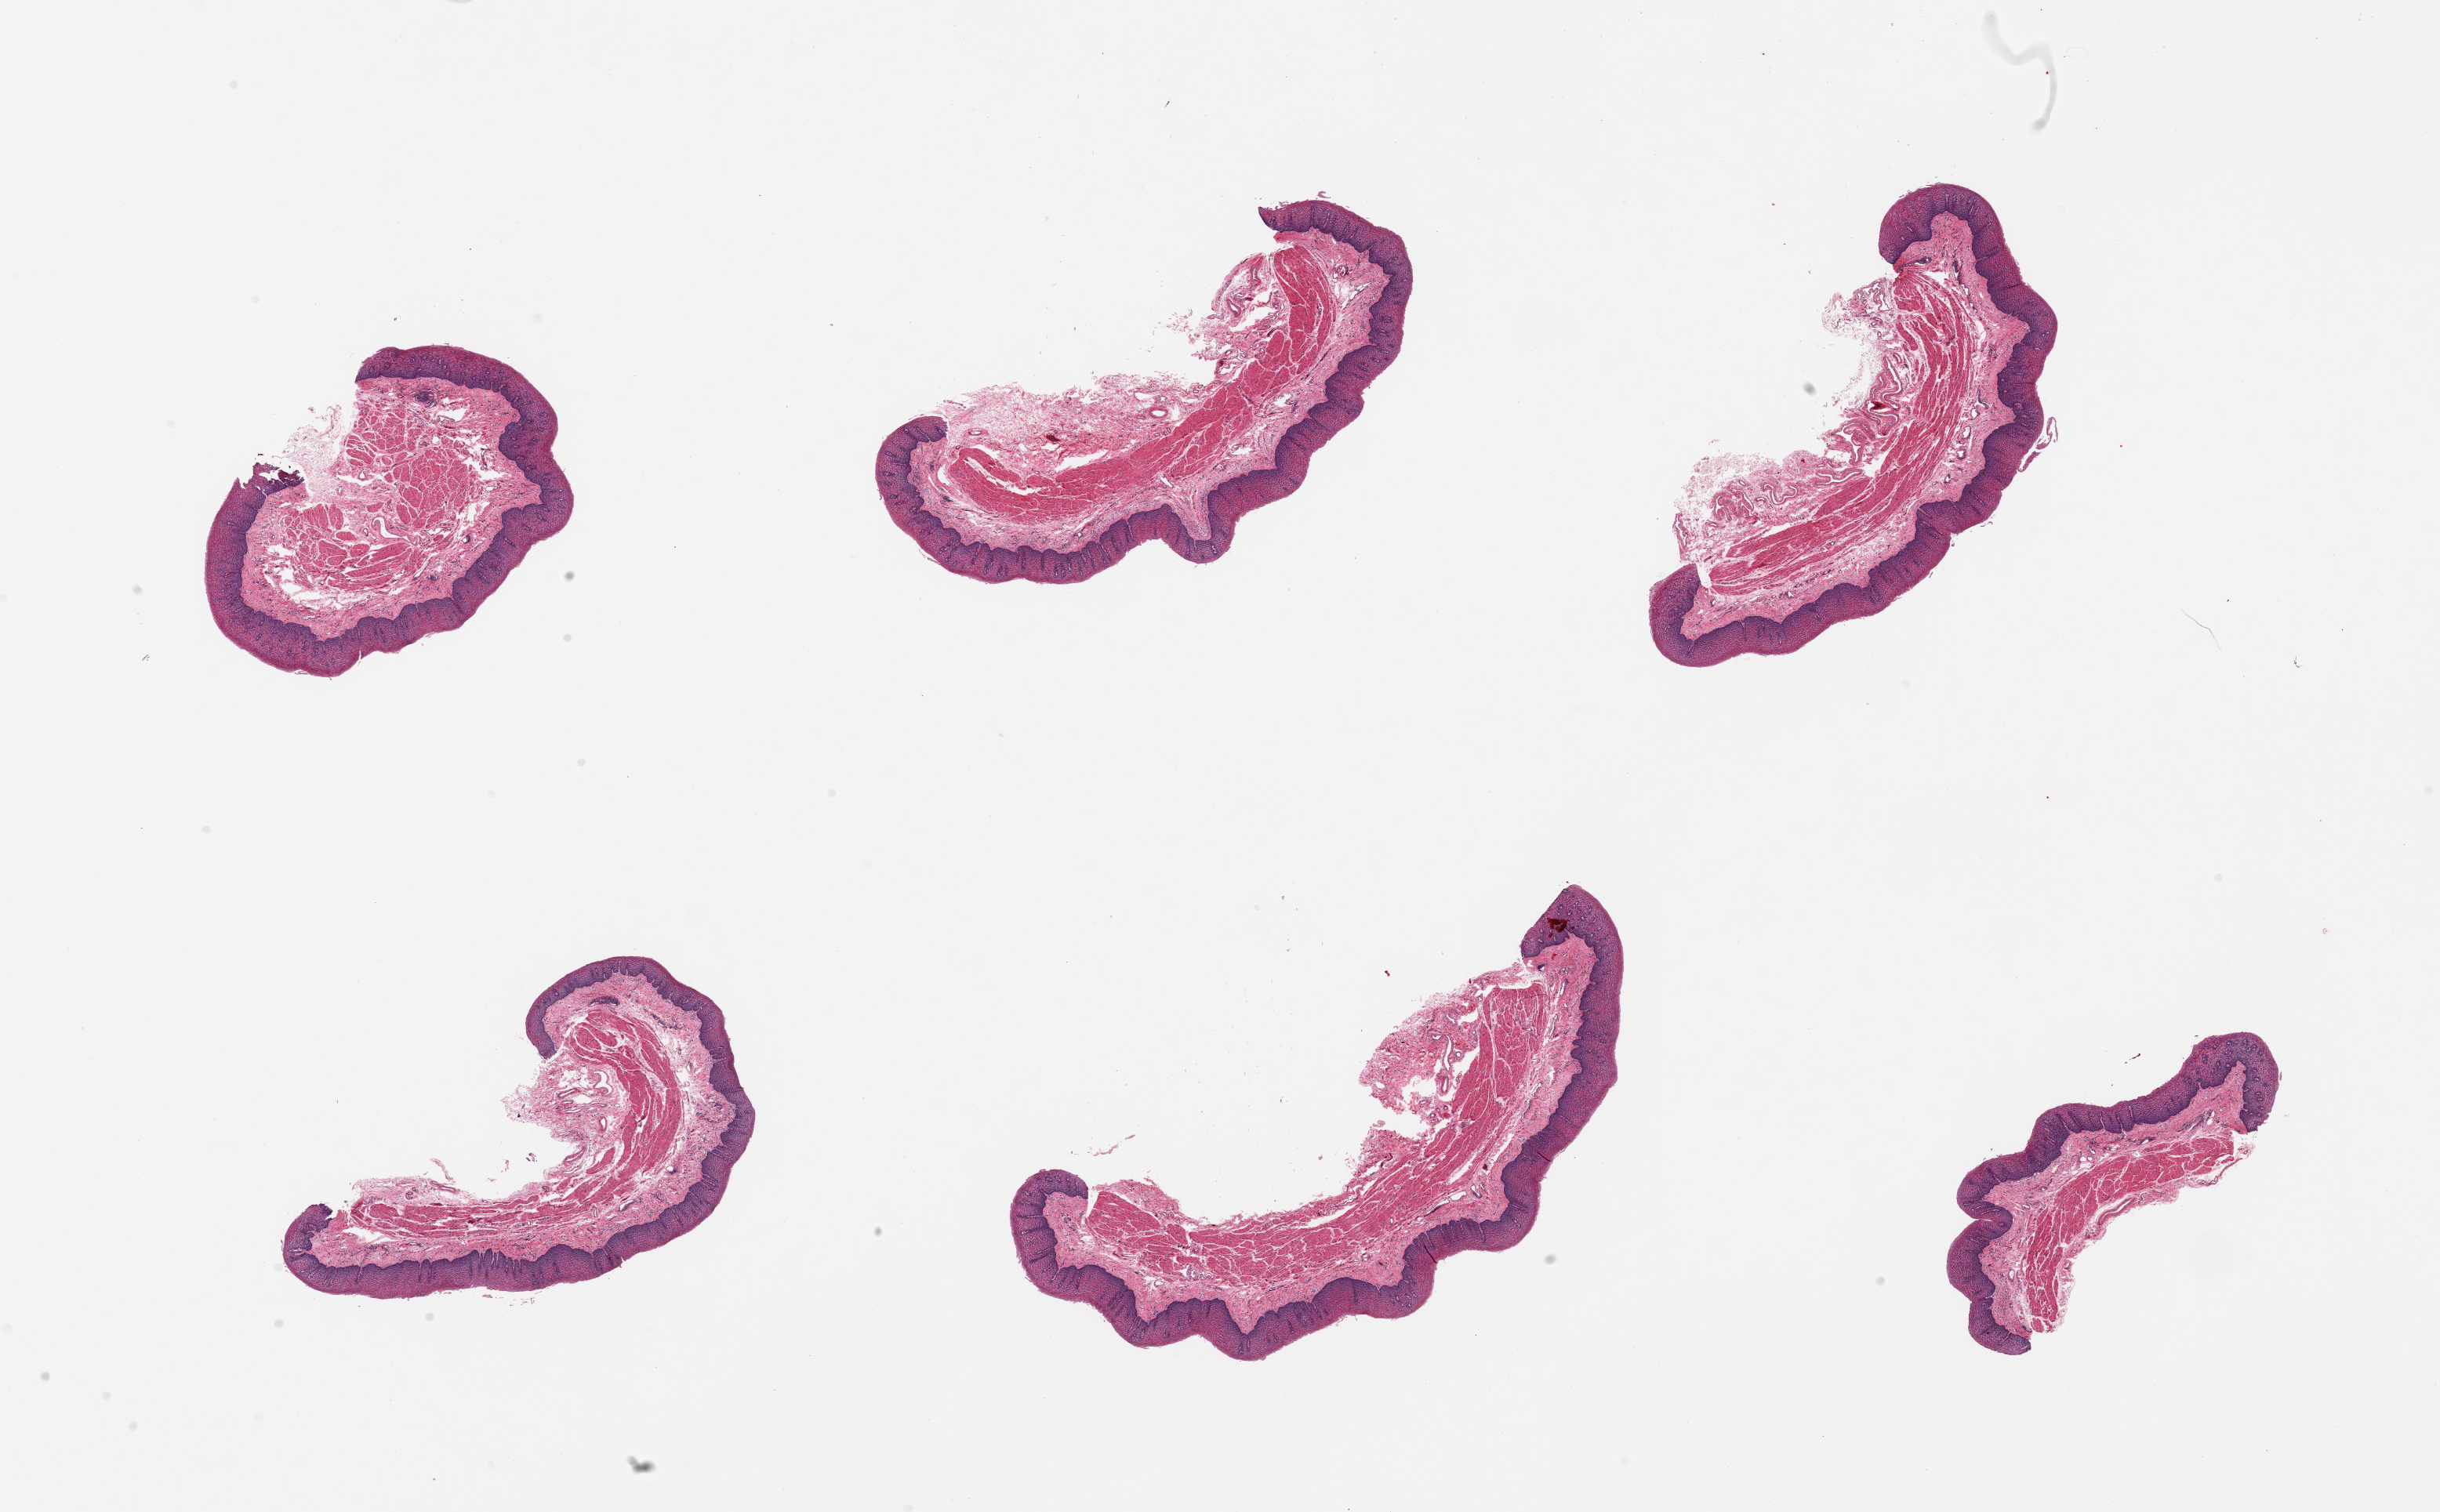
H&E whole-slide image — whole scanned area (about 24.6 x 15.3 mm) shown as a low-resolution overview. PAXgene-fixed paraffin-embedded (PFPE) section. Target tissue: esophageal mucous membrane. Tissue donor sample. Donor sex: female.
Review note (as recorded): 6 pieces; squamous mucosa up to 376 microns, well dissected.